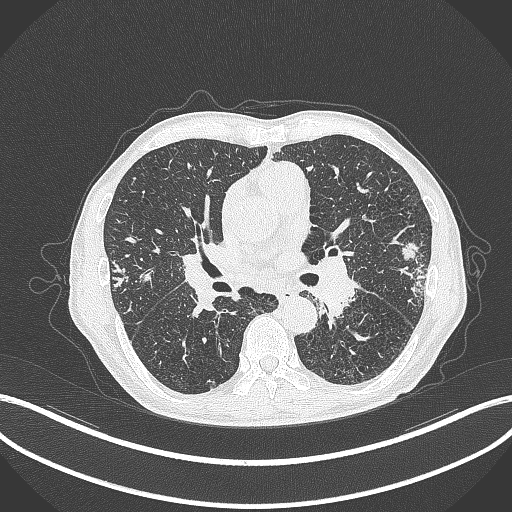
Chest CT, one axial slice. Slice 218 of 463 in the series (ordered by position). 120 kVp. Lung window (W 1500 / L -600 HU). 512 × 512 image matrix. Patient: male, 74 years. Case-level facts recorded for this patient, not image findings: clinical TNM (as recorded): T2a N1 M0.
Structures marked on this image (rectangle marked by the reading radiologist):
- lung tumour (recorded histology: adenocarcinoma): bounding box [x1, y1, x2, y2] px = [399, 236, 426, 268]